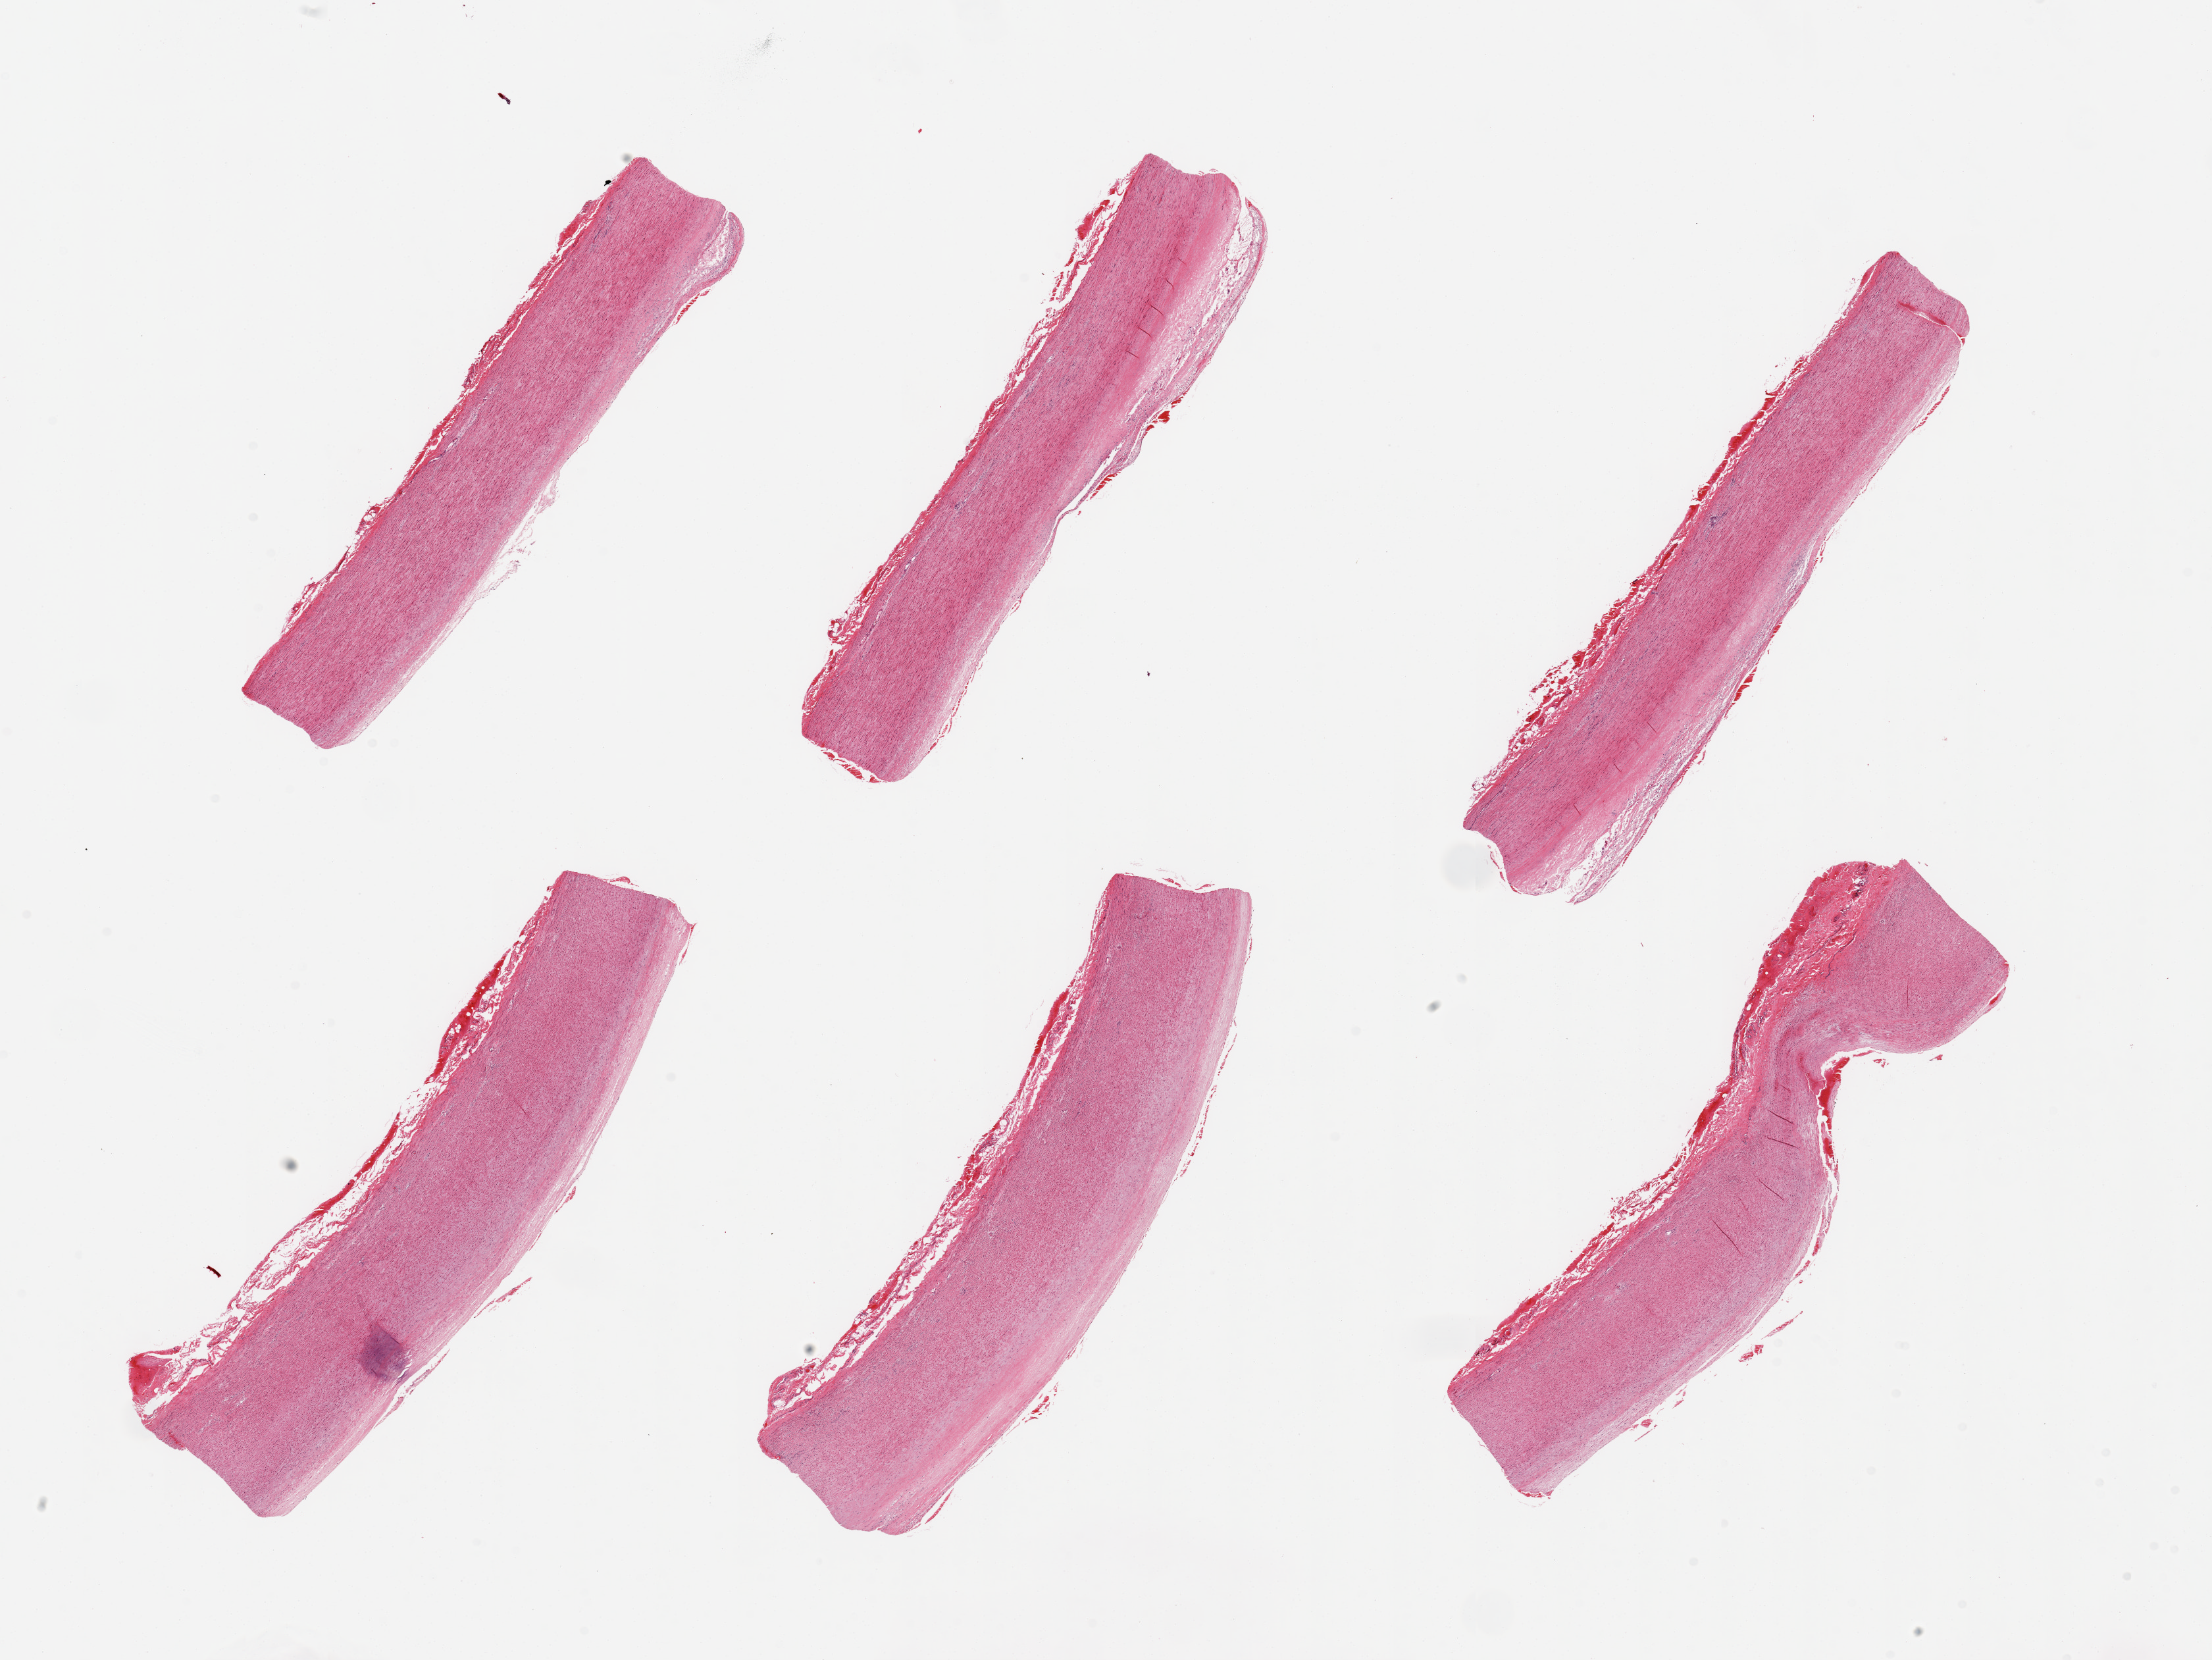
Haematoxylin and eosin whole-slide image, whole scanned area (about 26.6 x 19.9 mm) shown as a low-resolution overview. PAXgene-fixed paraffin-embedded (PFPE) section. Target tissue: aorta. Tissue donor sample. Donor sex: male.
Reviewer comment on this tissue sample: 6 pieces, atherosis of up to ~0.5mm.